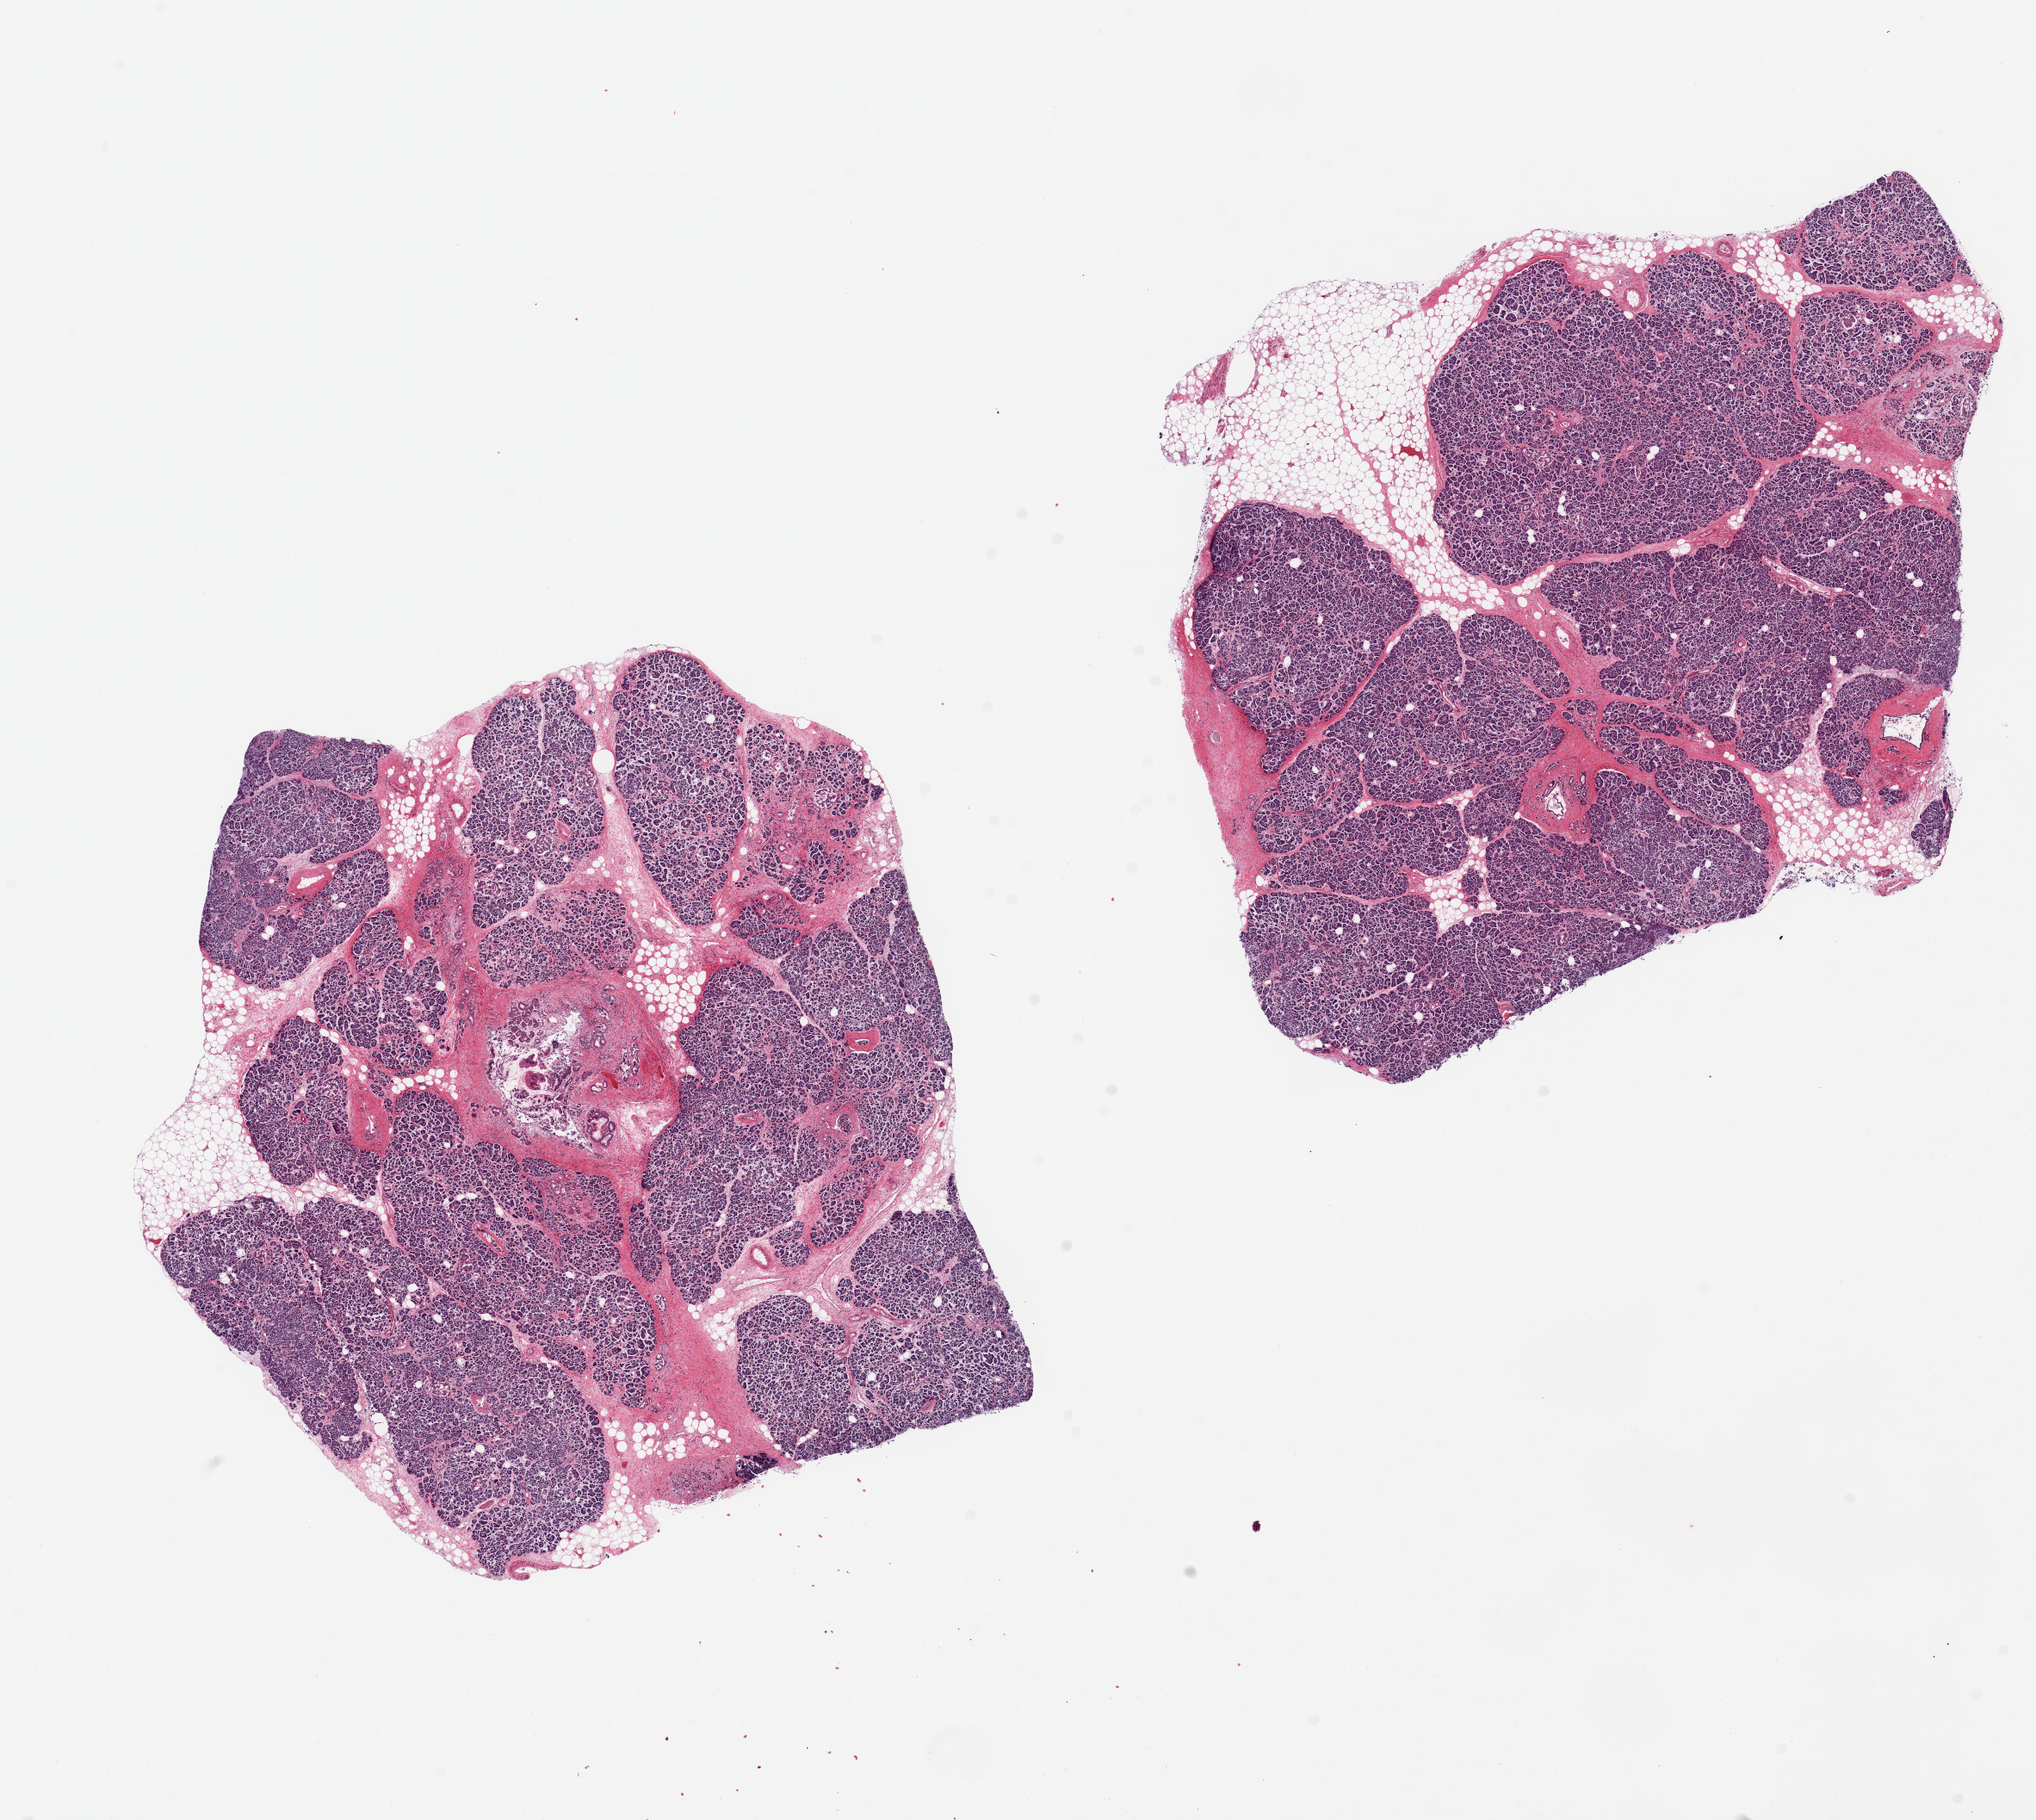
Digitized hematoxylin and eosin (H&E)-stained section, a low-resolution overview of the entire scanned area, about 18.7 x 16.7 mm. PAXgene-fixed paraffin-embedded (PFPE) section. Target tissue: pancreas. Tissue donor sample. Donor sex: male.
Pathologist's review note for this sample: 2 pieces, 8x8 & 7x7mm; 10 and 20% adipose, external and internal.